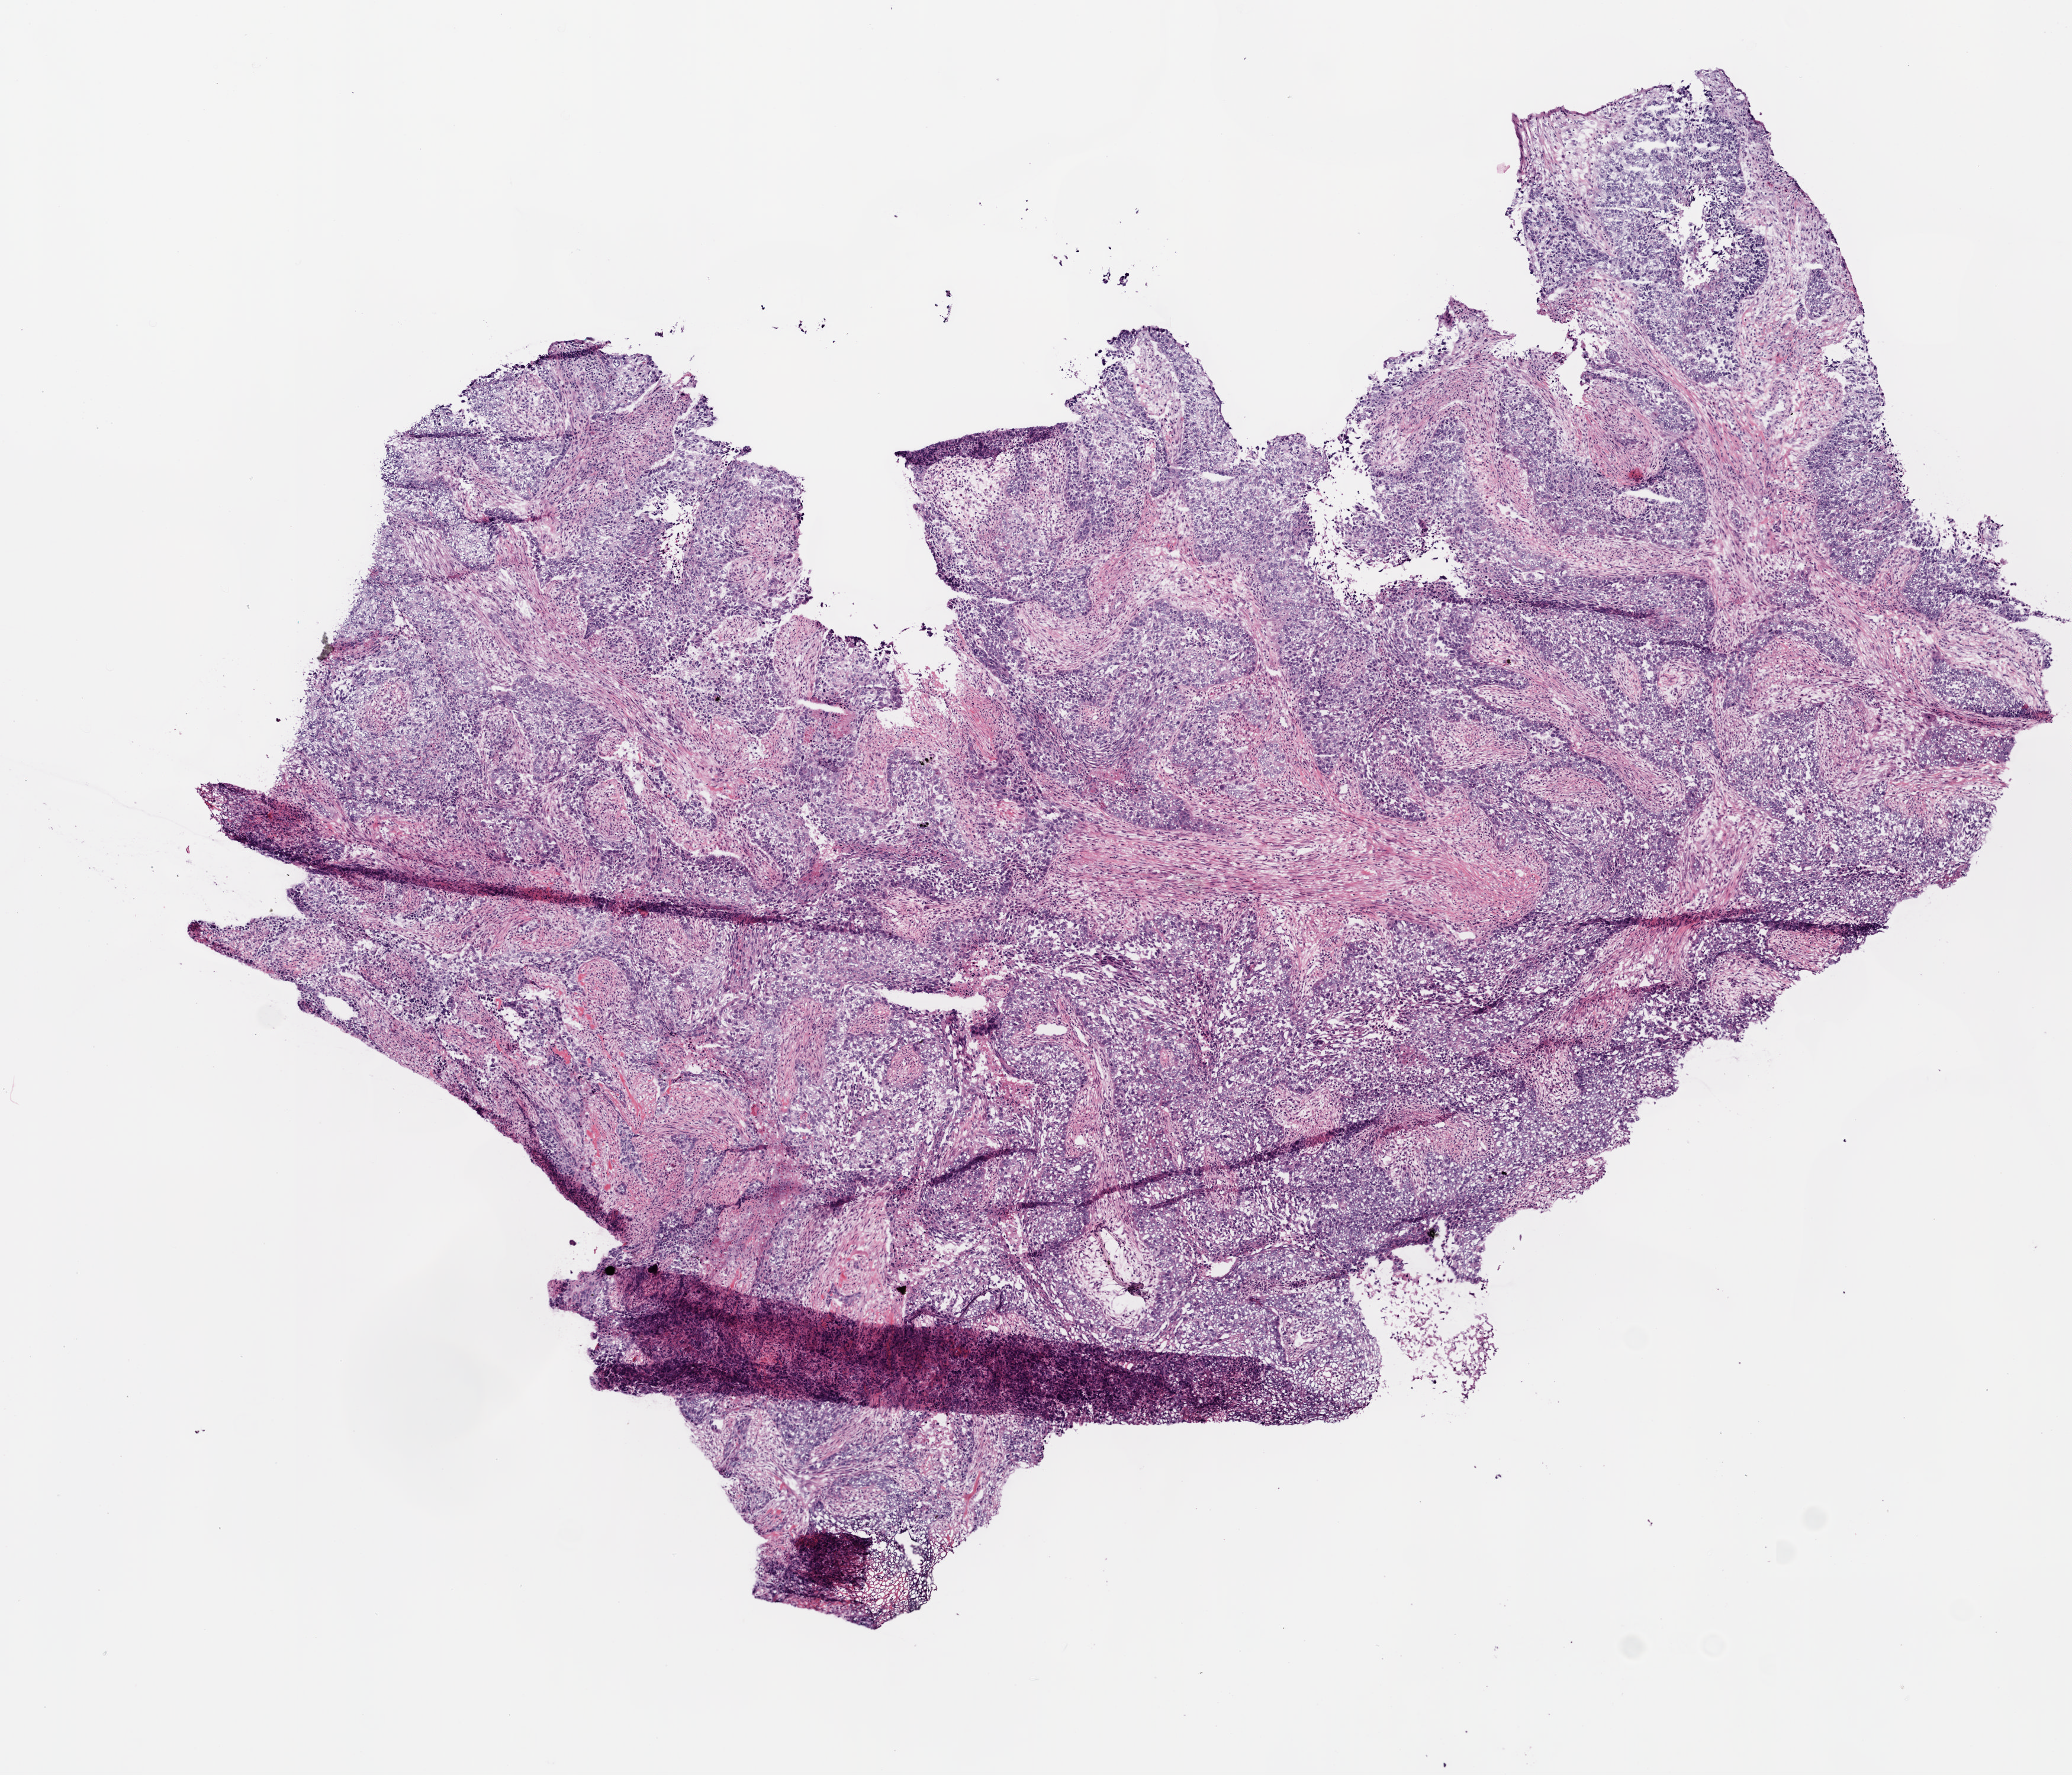
Digitized Hematoxylin and eosin (H&E) stained tissue section (whole slide) — shown as a low-resolution overview of the whole scanned area (about 7.0 x 6.0 mm); frozen section from the bottom of the tissue portion; sample: primary tumour, lung. Patient: male, age at initial diagnosis 77 years. Composition of this section per pathologist review: tumour cells 70%, tumour nuclei 75%, normal cells 0%, stromal cells 20%, necrosis 10%.
AJCC pathologic stage: IIA (7th edition). Pathologic diagnosis: Squamous cell carcinoma, NOS.